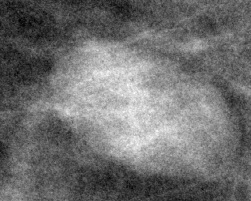
Region of interest cut from a scanned film mammogram (one marked finding), right breast, MLO view.
Finding: mass, shape oval, margins circumscribed; BI-RADS assessment category 3; benign; no additional work-up was recommended (benign without callback).